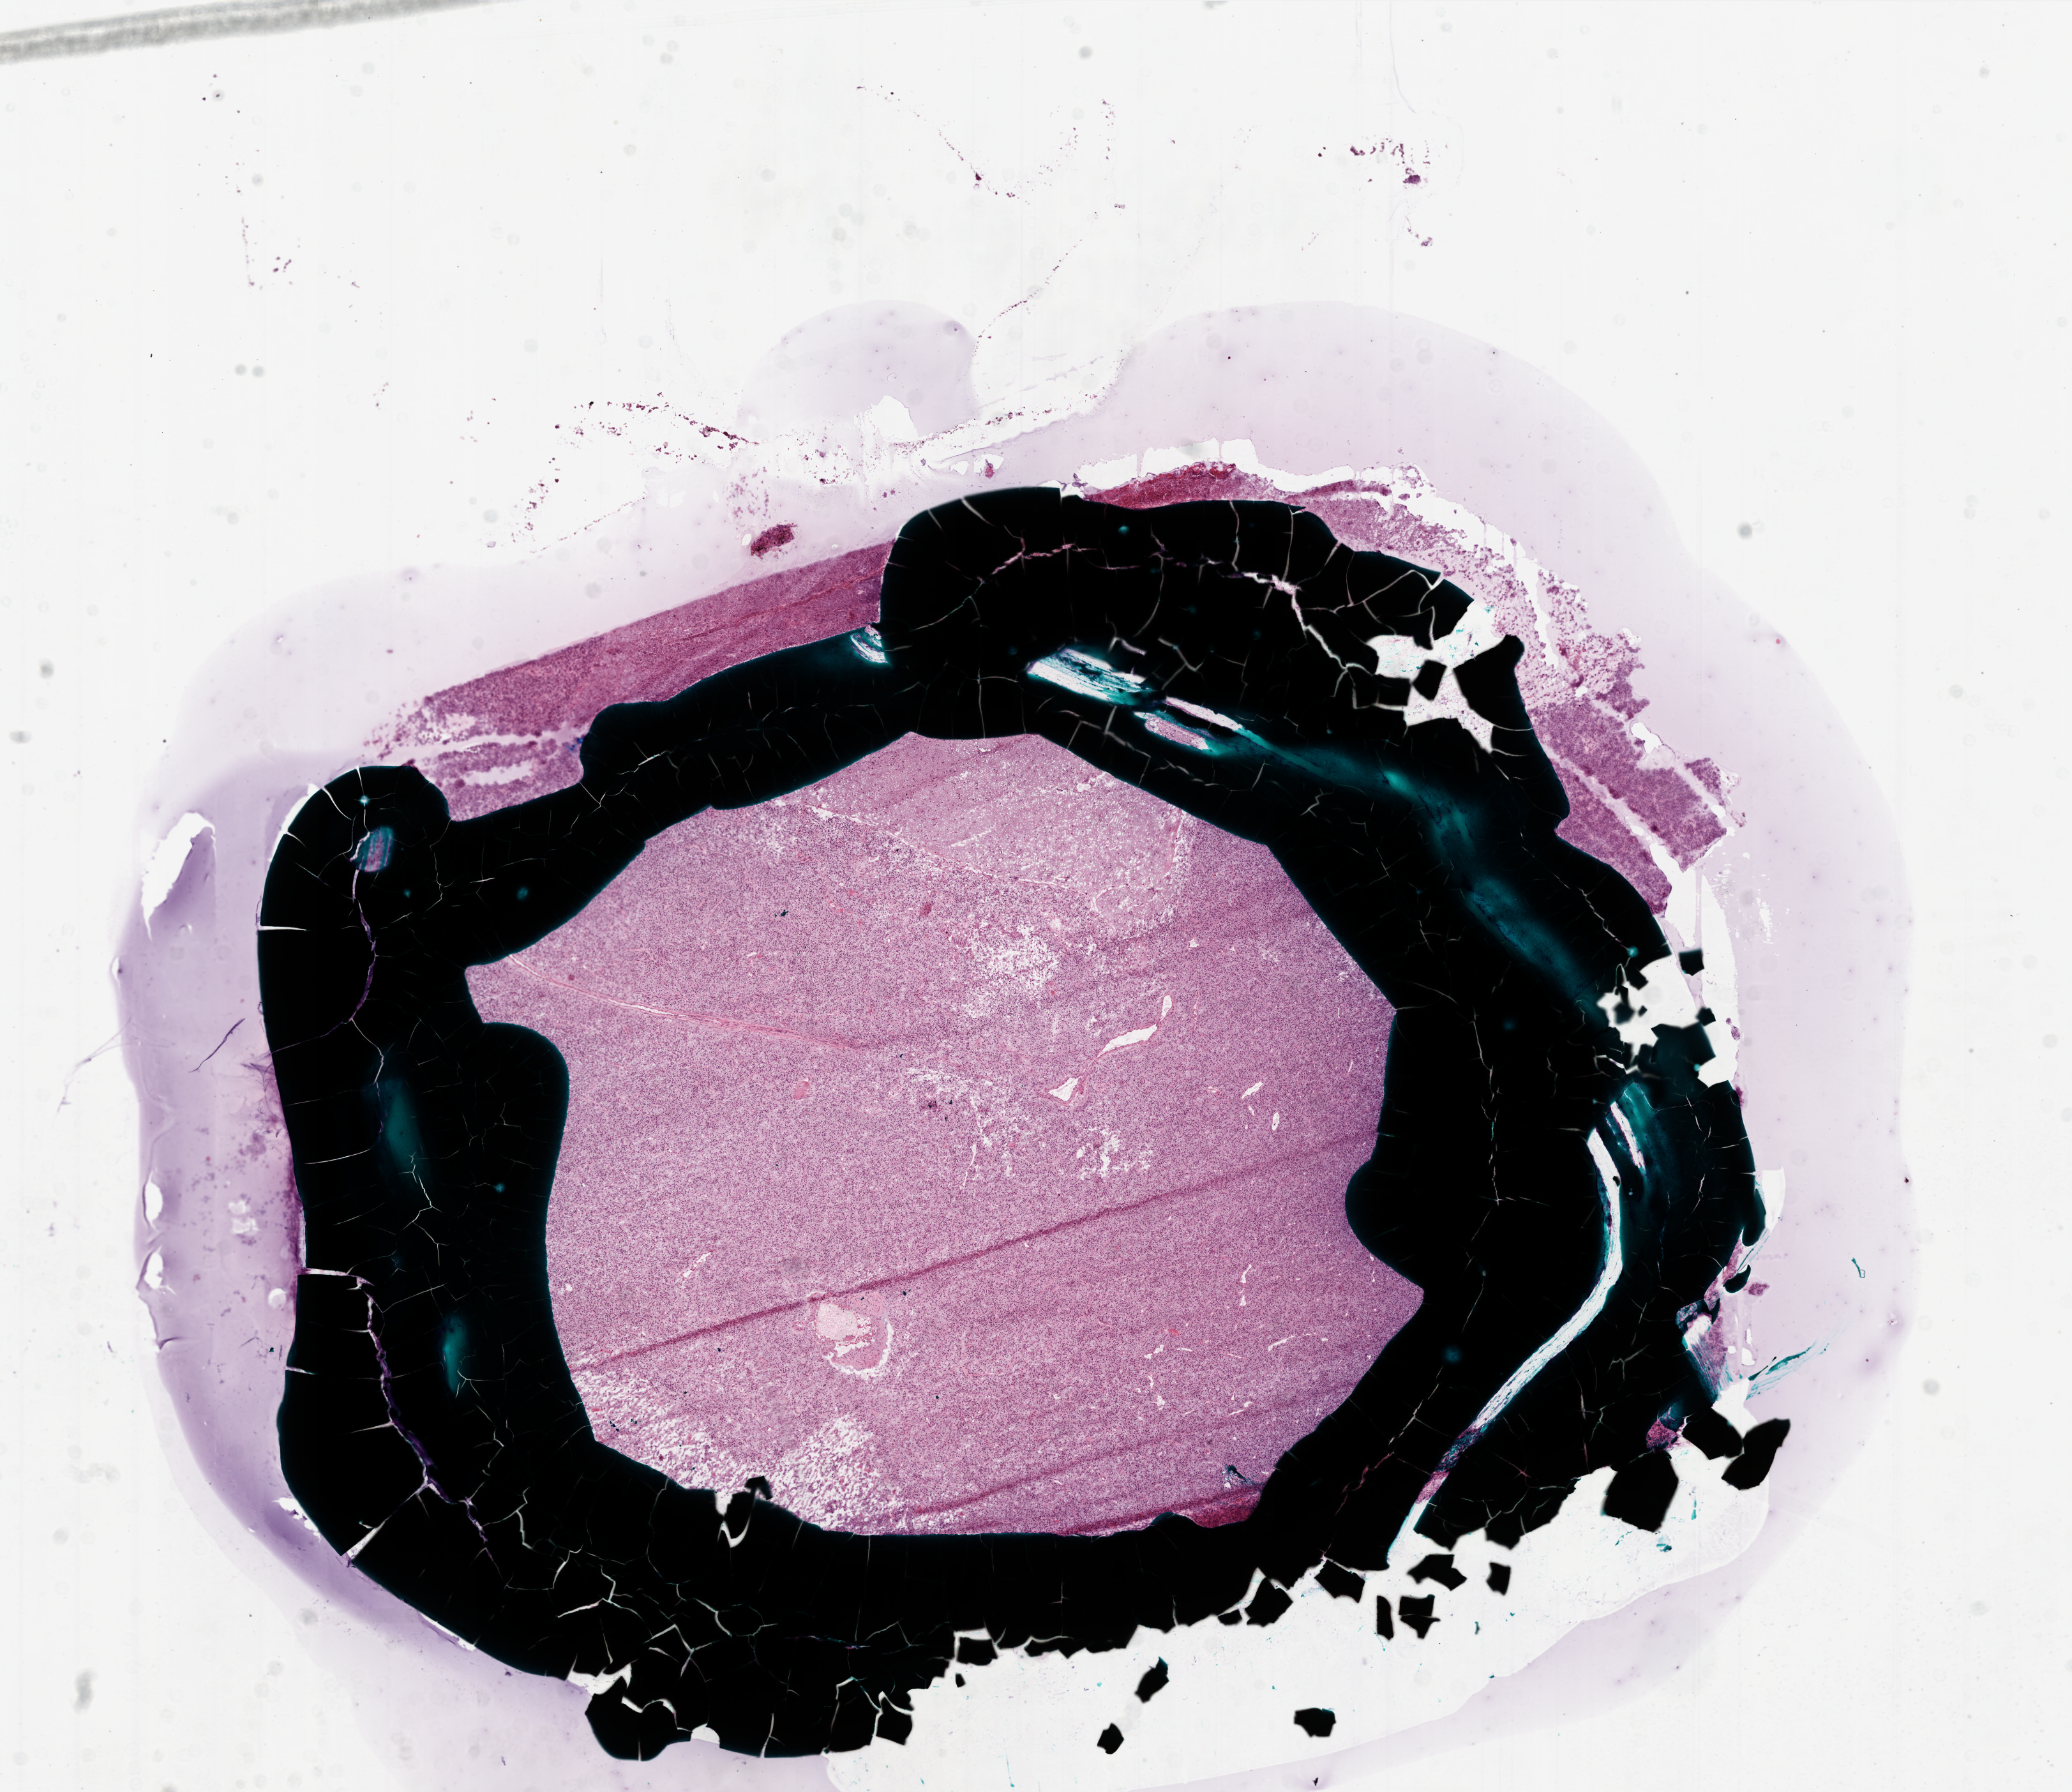
Digitized H&E-stained tissue section (whole slide) — low-resolution overview of the scanned area, about 13.0 x 11.2 mm. Frozen section. Primary tumour sample from the brain. Female, age 63 years at initial diagnosis. Pathologist review of this section (percent, as recorded): tumour cells 80%, tumour nuclei 95%, normal cells 0%, stromal cells 15%, necrosis 5%. Inflammatory infiltration, as recorded: lymphocyte infiltration 0%, monocyte infiltration 0%, neutrophil infiltration 0%.
Pathologic diagnosis: Glioblastoma.